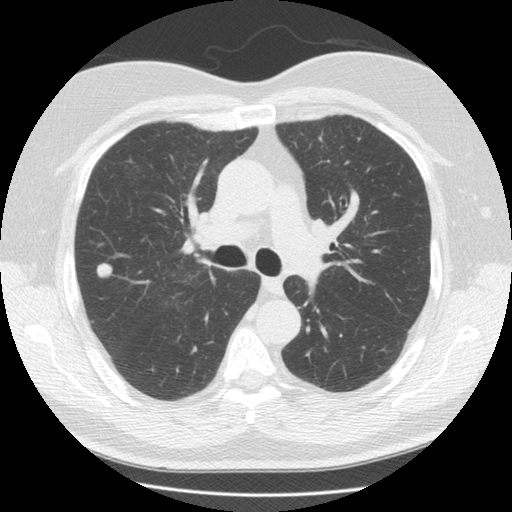
Axial slice from a low-dose chest CT screening exam; third annual screen; lung window (W 1500 / L -600 HU). Male participant, aged 65 years at enrolment. Former smoker at enrolment.
Expert-annotated lung lesion, bounding box <91,257,118,285> (left, top, right, bottom; pixels). The exam's reader record, not a measurement of the box and not confirmed to be the same lesion: non-calcified nodule or mass ≥4 mm, right upper lobe, 12 × 12 mm, smooth margins, soft tissue attenuation, pre-existing on the prior screen: yes; interval growth: yes.